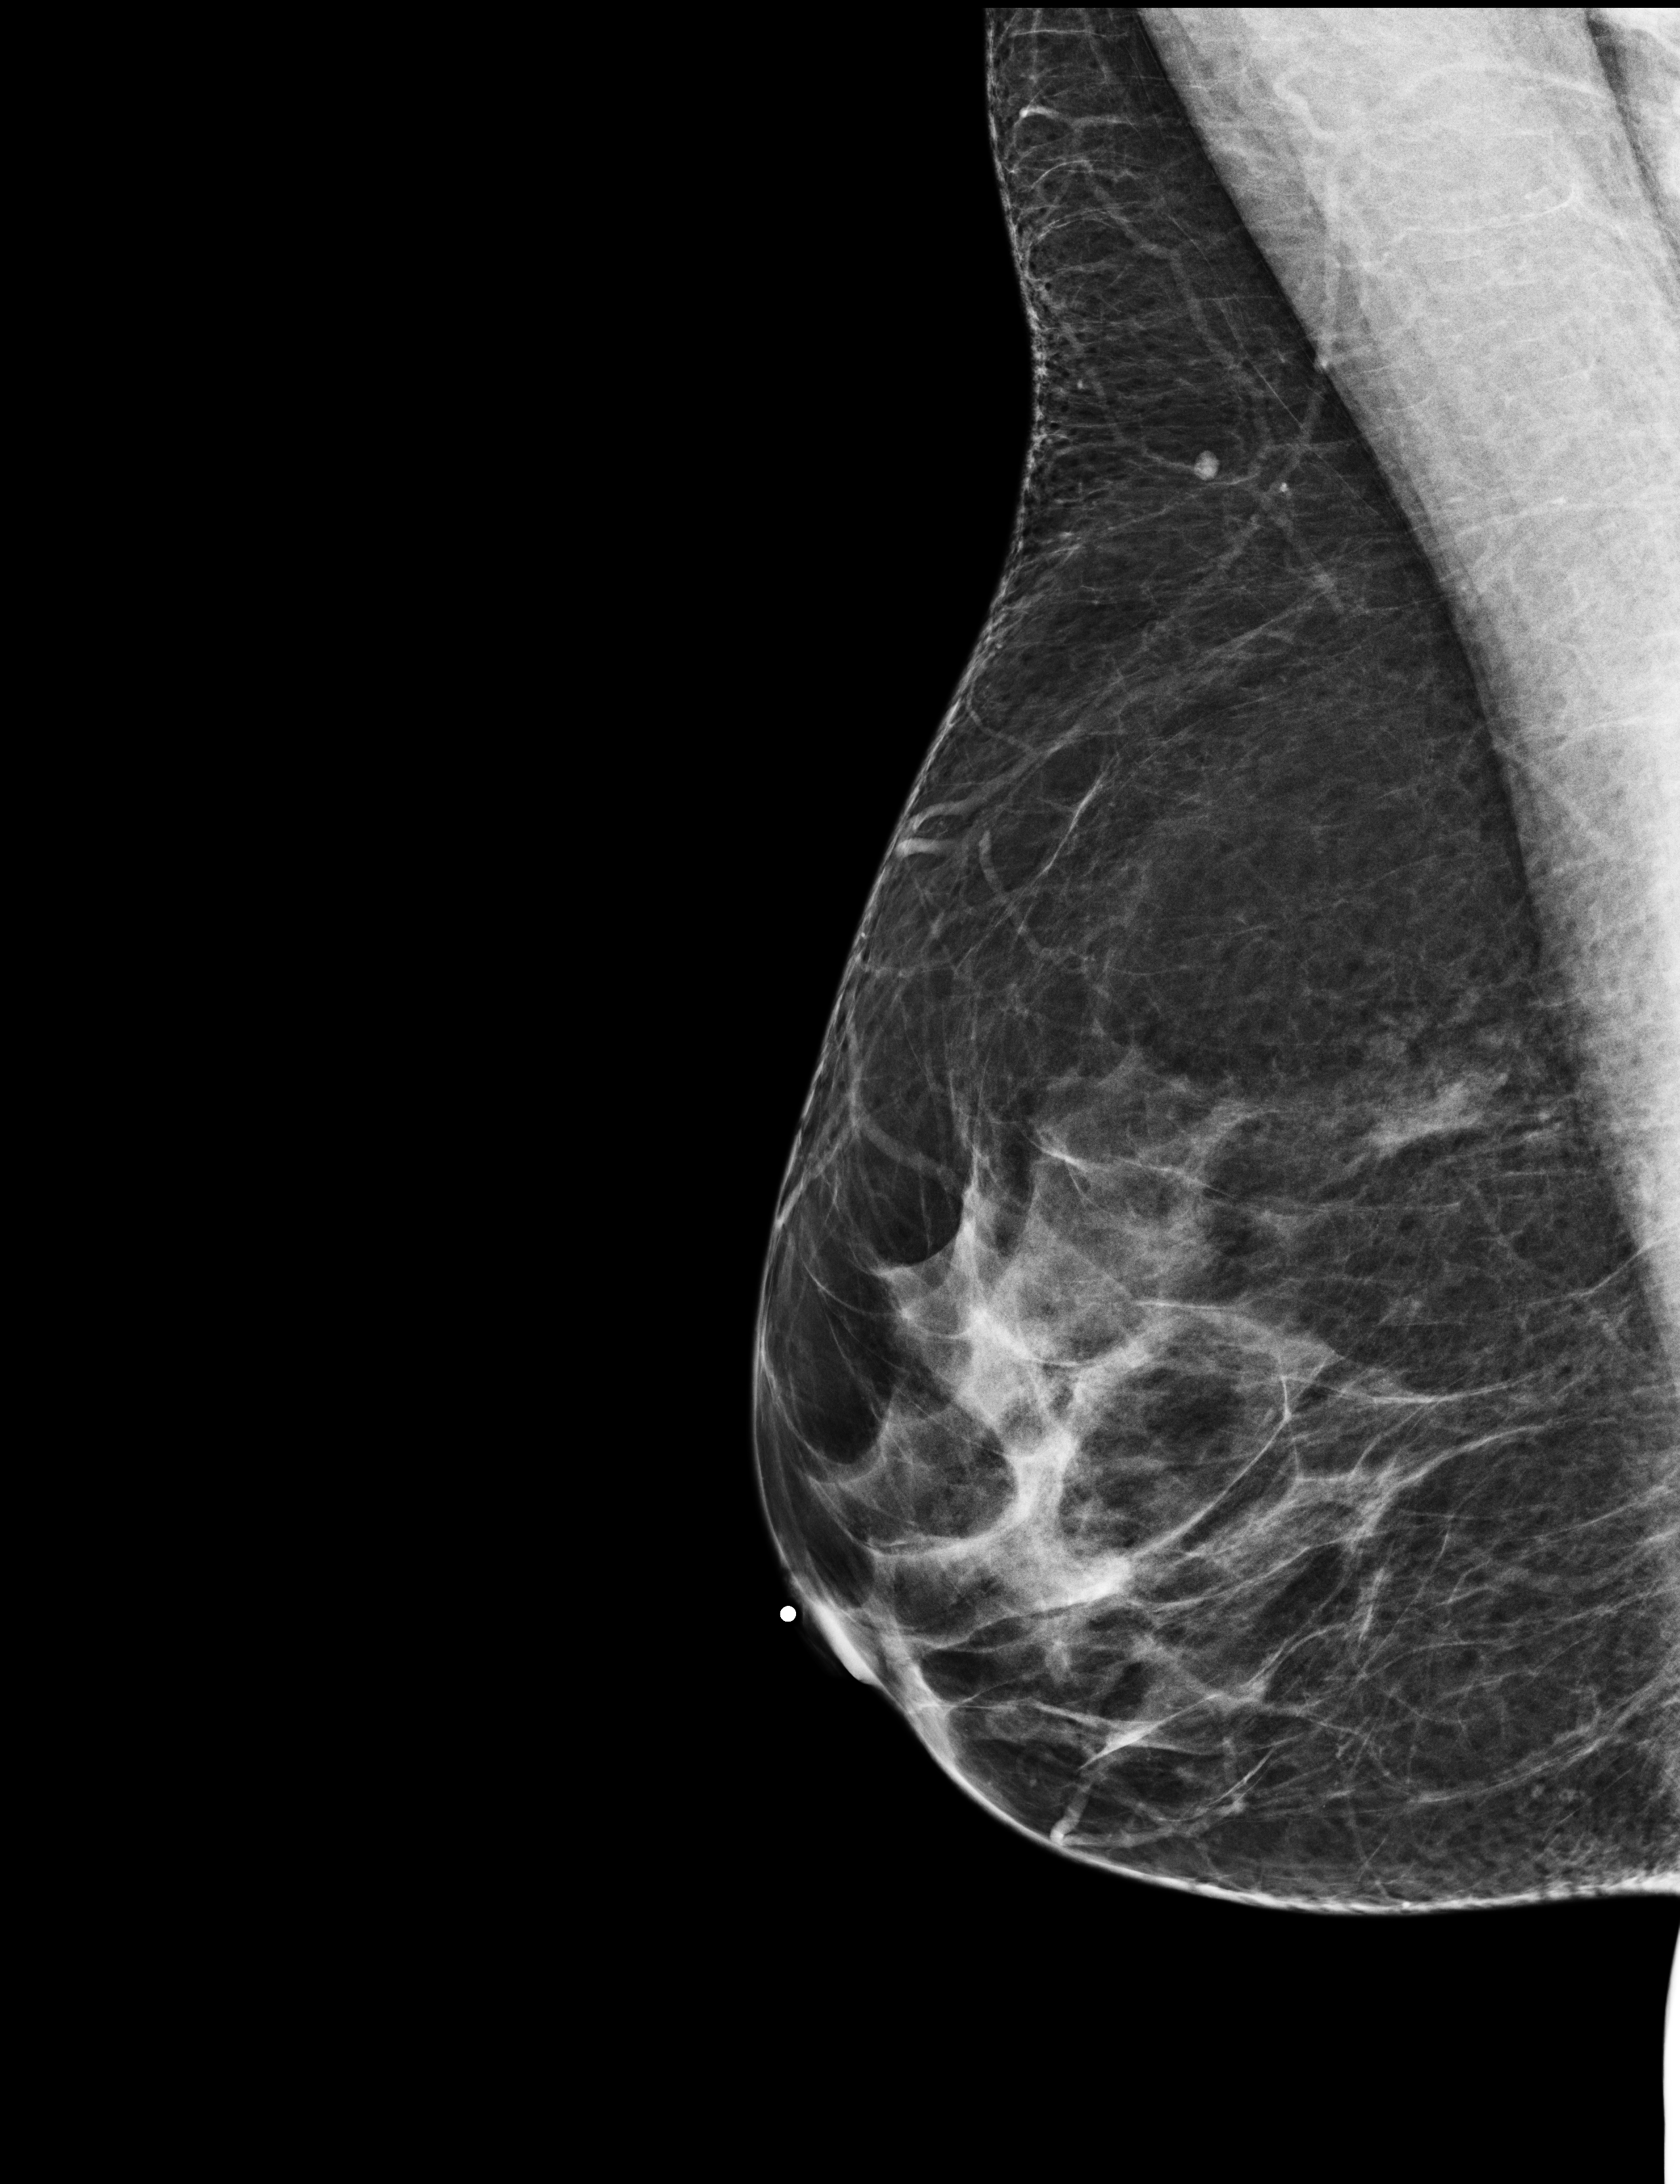
Screening examination; compressed breast thickness 67 mm. Female patient, age 50 years.
Image type: full-field digital mammogram. Breast: right. Projection: MLO view.